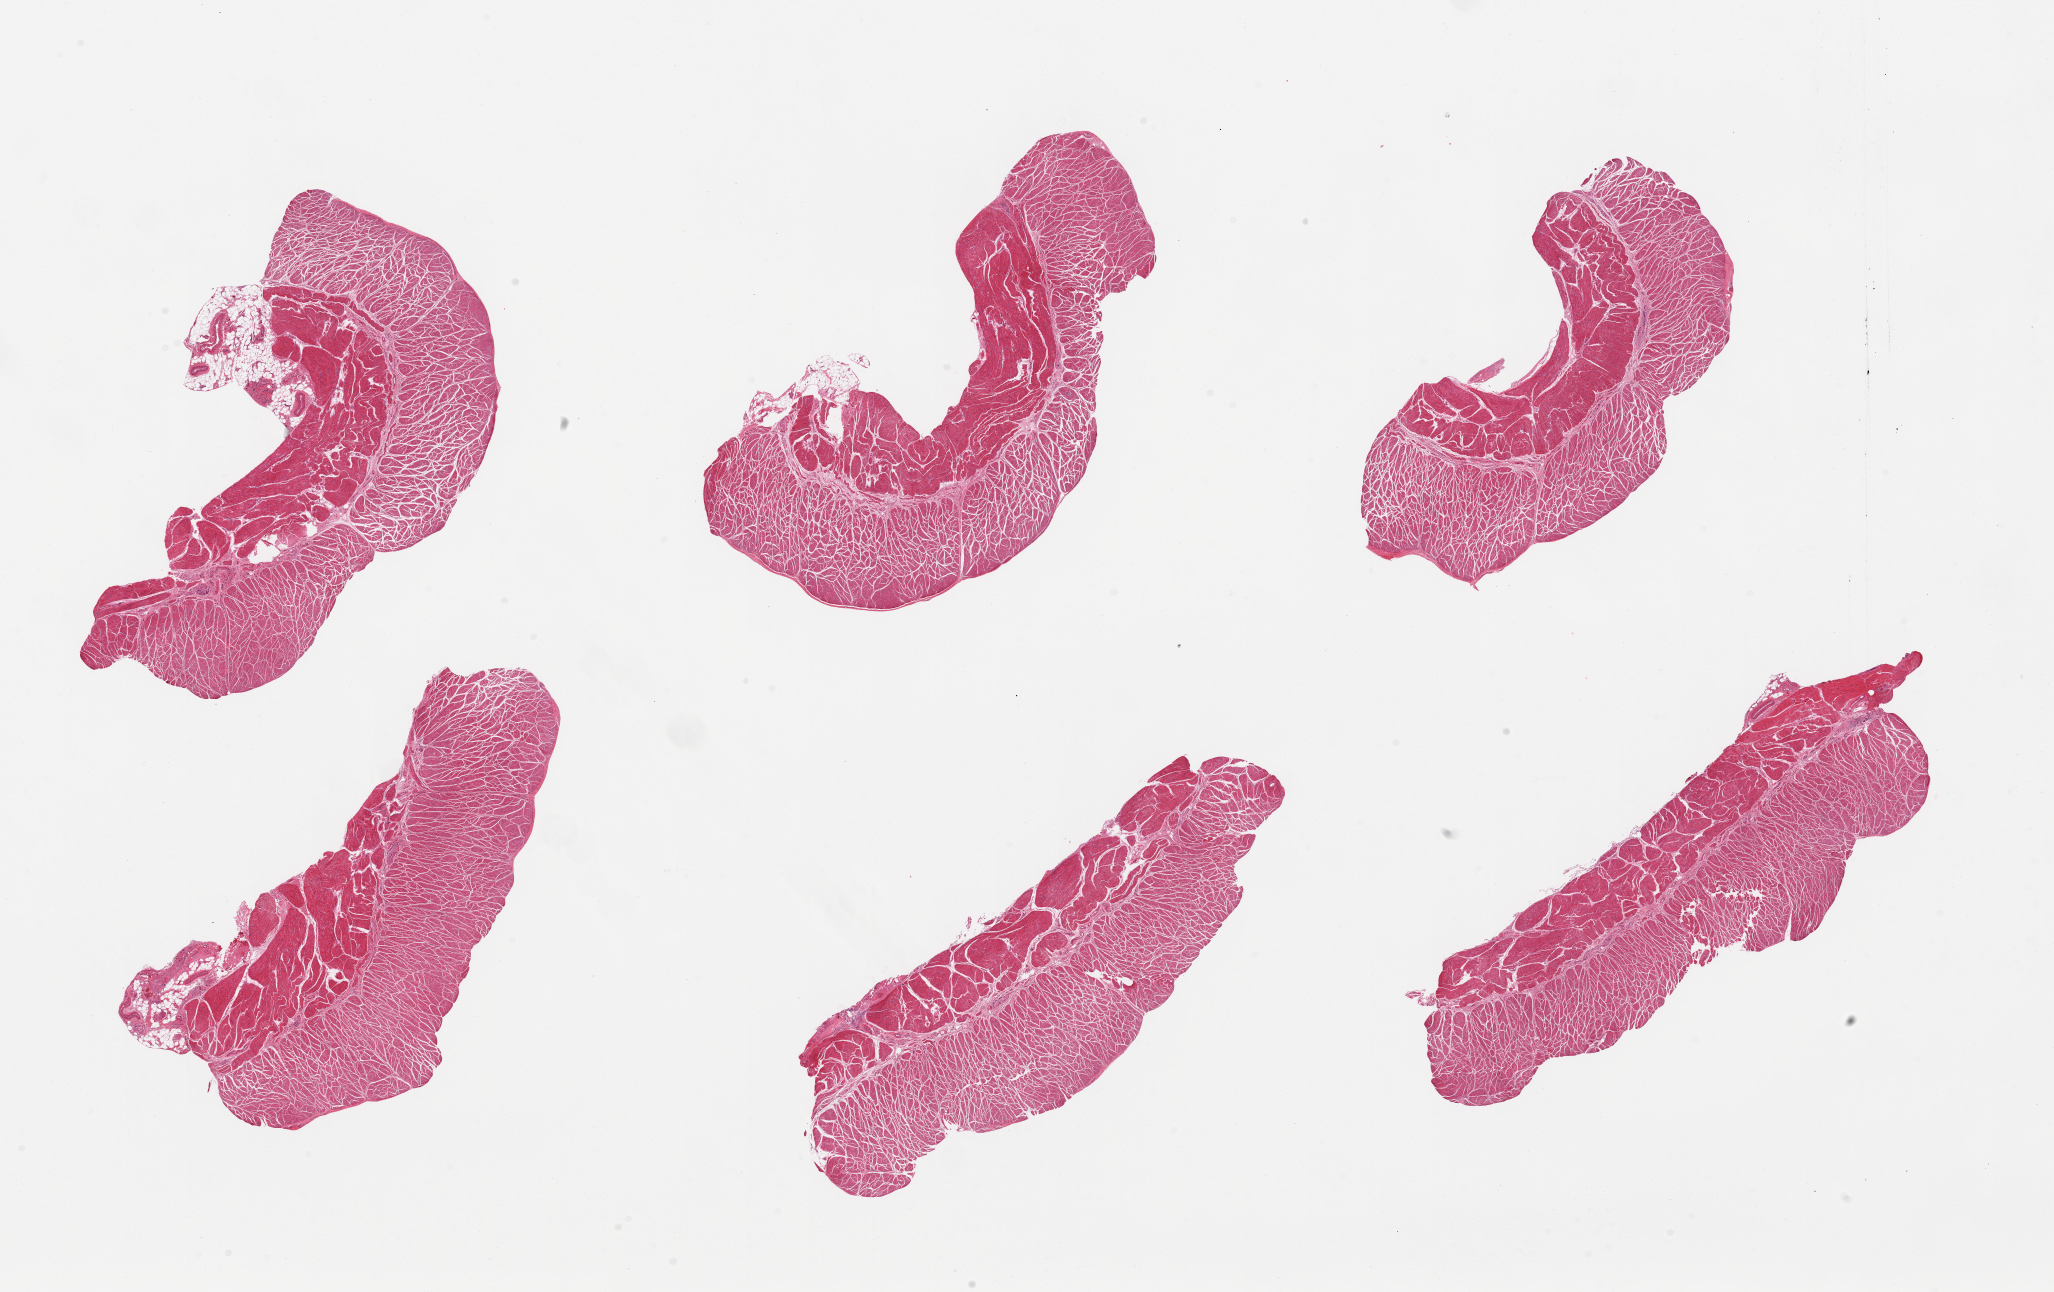
Hematoxylin and eosin (H&E) whole-slide image, brightfield — a low-resolution overview of the entire scanned area, about 32.5 x 20.4 mm (slide scanned at 20x), PAXgene-fixed, paraffin-embedded tissue, target tissue: gastroesophageal junction, tissue donor sample.
• review note (as recorded): 2 pieces all muscularis, good specimens